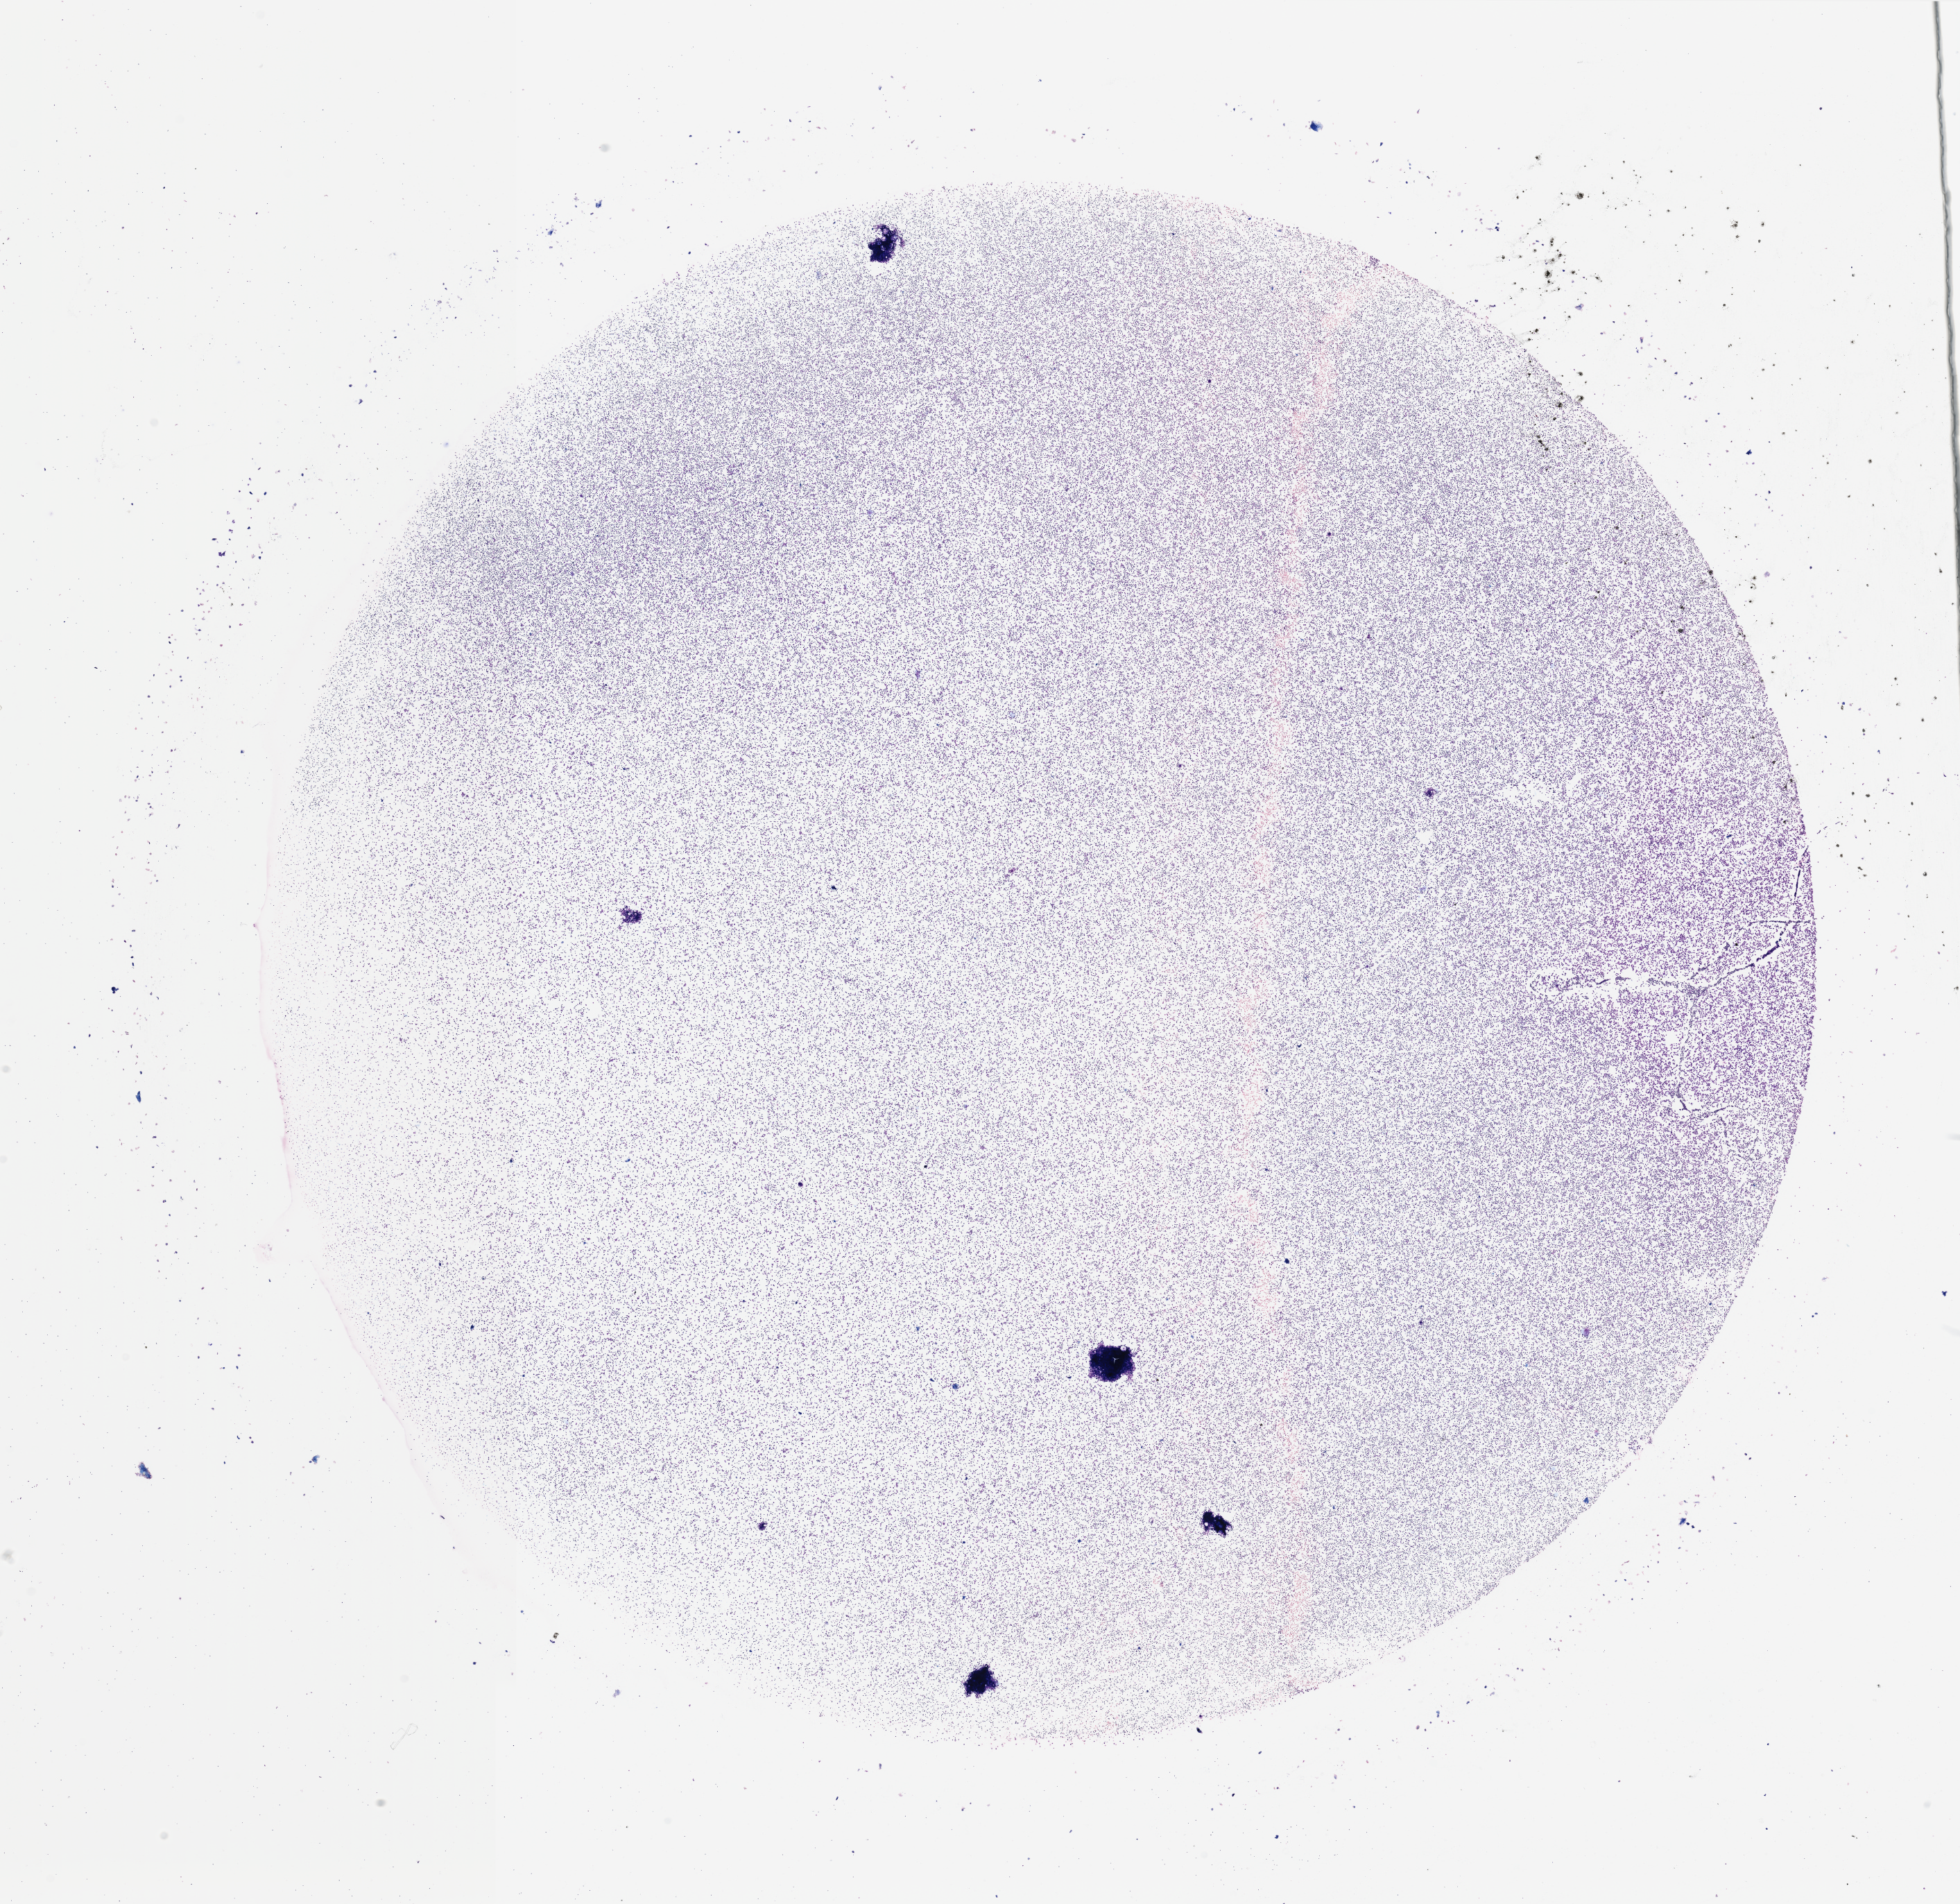
Hematoxylin and eosin (H&E) stained whole-slide image, a low-resolution overview of the entire scanned area, about 22.3 x 21.7 mm, bone marrow (leukaemic) sample. Patient: female, age 62 years.
Diagnosis: Acute Myeloid Leukemia.